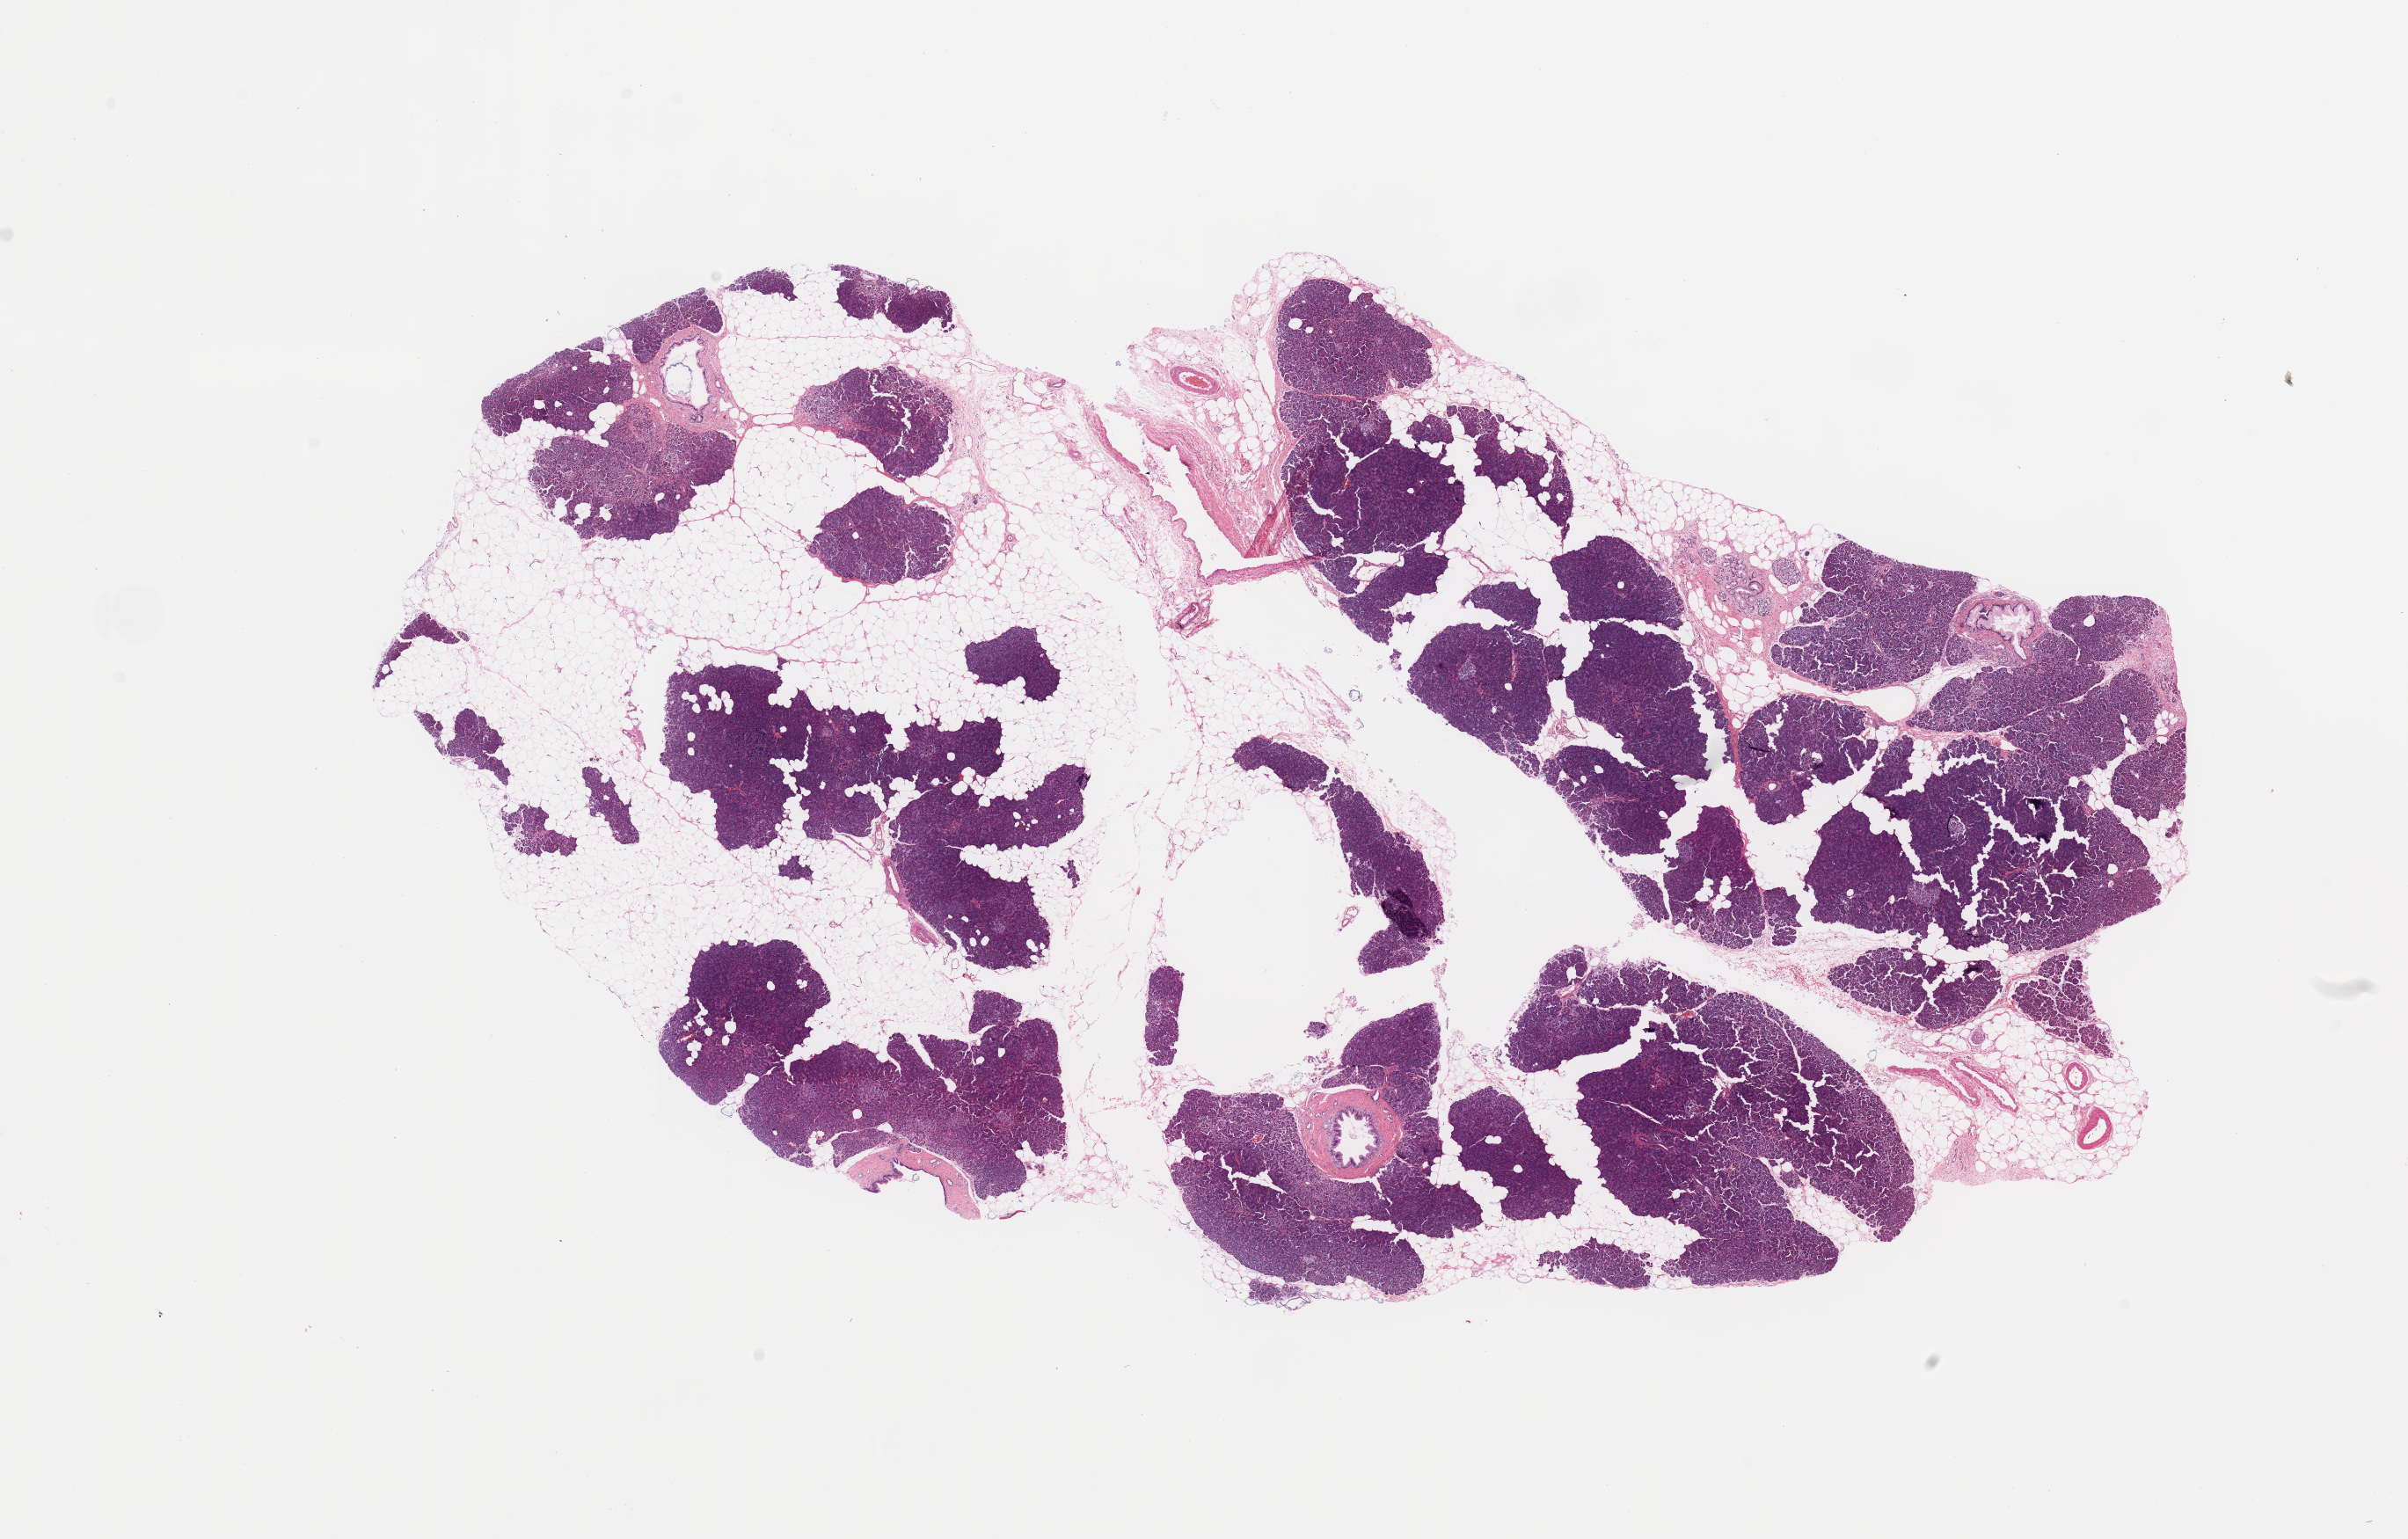
Digitized H&E tissue section (whole slide) — a low-resolution overview of the entire scanned area, about 21.7 x 13.8 mm (from a 20x scan), normal (non-tumour) tissue sample, sampled site: pancreas. Patient: female, age 60 years.
This section: normal (non-tumour) tissue from the same patient. Patient diagnosis: Infiltrating duct carcinoma, NOS.